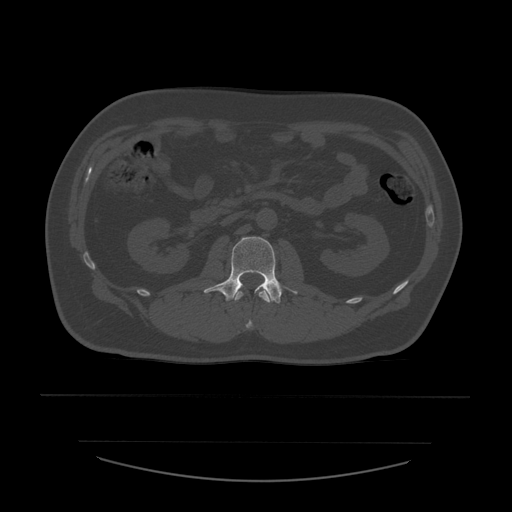
CT including the spine, one axial slice. Position 206 of 532 along the scan axis. Bone window (W 1800 / L 400 HU). 512 × 512 image matrix, field of view 441 × 441 mm. Patient age 44 years. Case-level facts recorded for this patient, not image findings: primary cancer: soft tissue sarcoma.
Annotated regions visible in this slice (semi-automatic segmentation, software-assisted and operator-edited):
- L1 vertebra: bounding box <234,290,273,329> (left, top, right, bottom; pixels)
- L2 vertebra: <204,237,298,304>